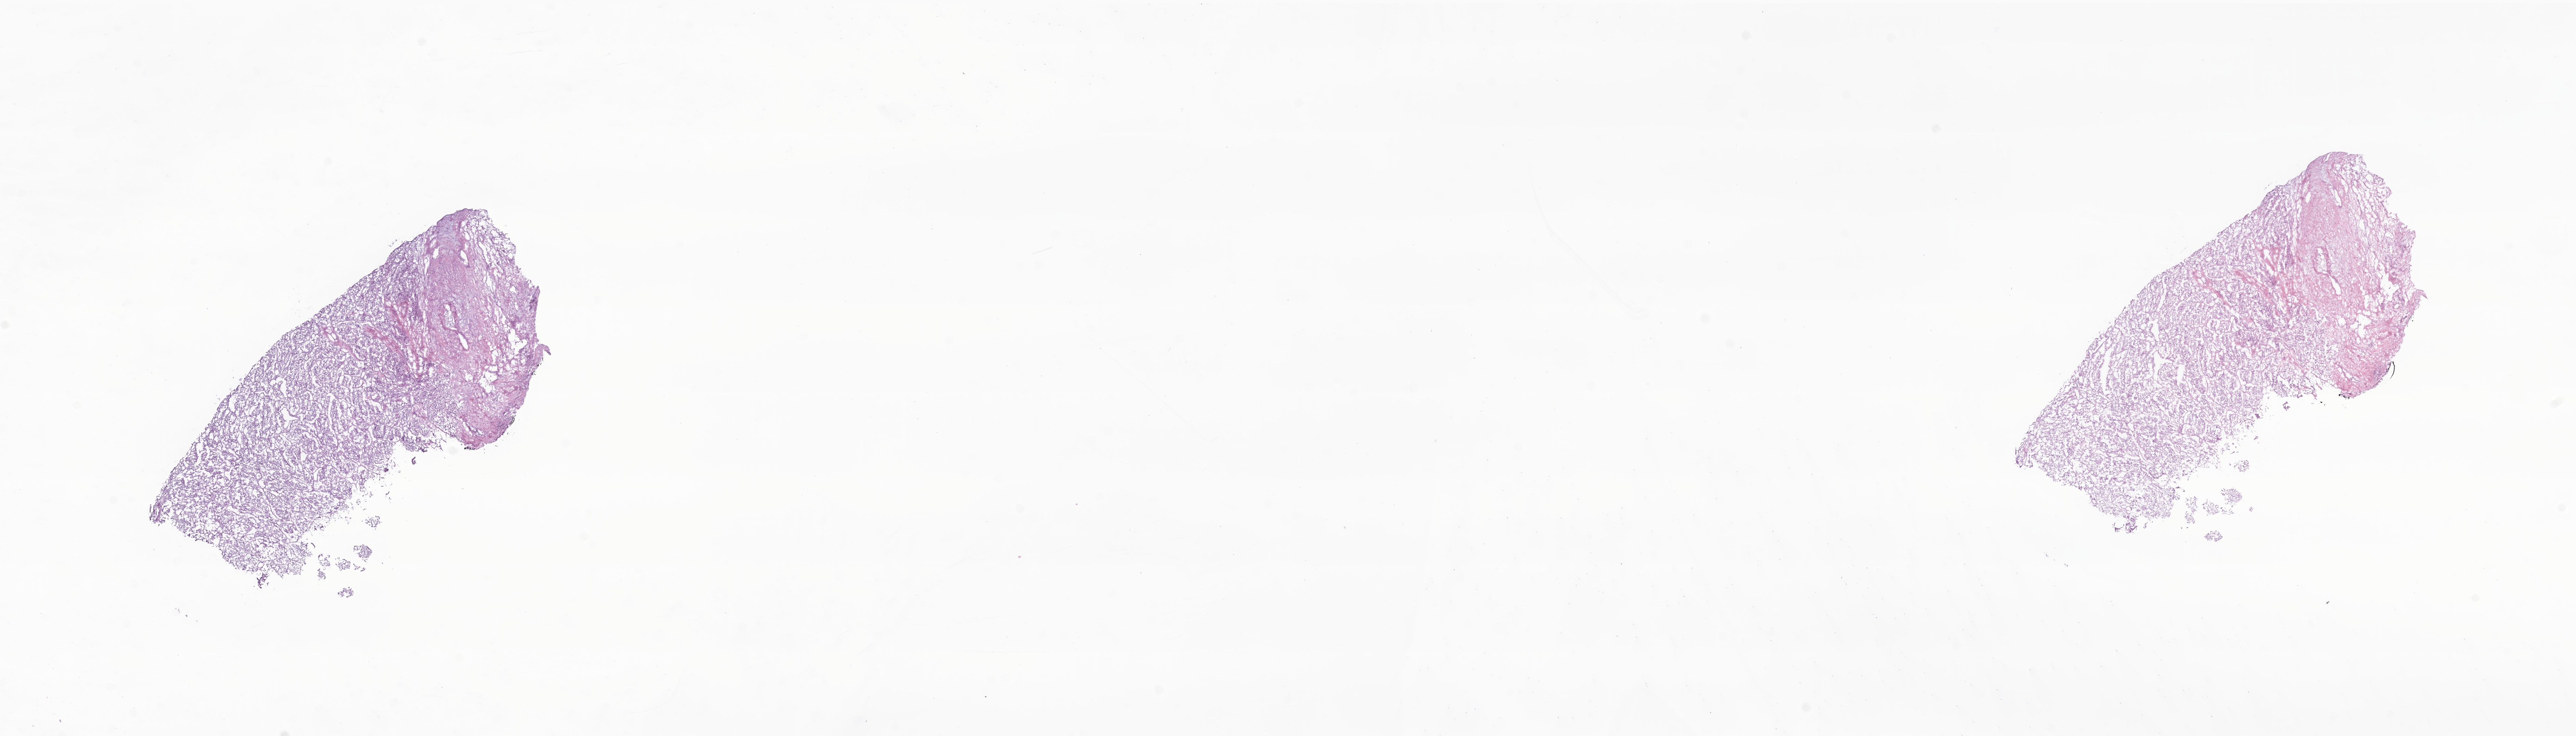
Digitized hematoxylin and eosin (H&E)-stained section of tumor tissue from the kidney — low-resolution overview of the scanned area, about 31.7 x 9.1 mm, frozen section. Female patient, age 81 months (6 years 9 months).
- diagnosis: Paraganglioma, NOS